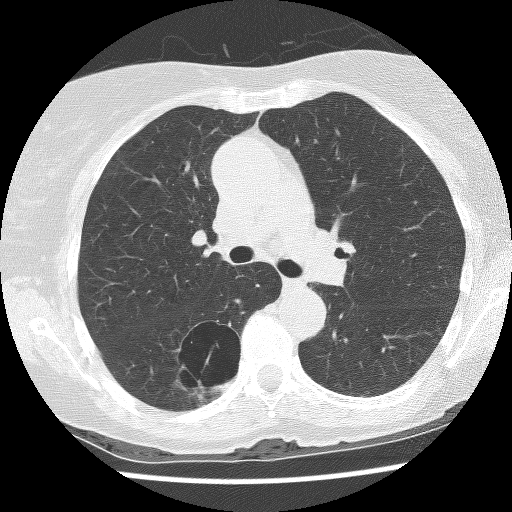
Chest CT (low-dose screening protocol), one axial image. Baseline annual screen. Lung window (W 1500 / L -600 HU). 2.5 mm slice thickness. Female participant, aged 69 years at enrolment. Former smoker at enrolment.
Expert-annotated lung lesion, bounding box <162,321,245,396> (left, top, right, bottom; pixels). The screening reader recorded 2 non-calcified nodules or masses ≥4 mm on this exam (right lower lobe, right lower lobe); which of them this box marks is not recorded. Lung cancer was diagnosed 288 days after this screen: non-small cell carcinoma, right lower lobe, poorly differentiated (G3), stage IB (AJCC 6th edition), 36 mm at pathology.